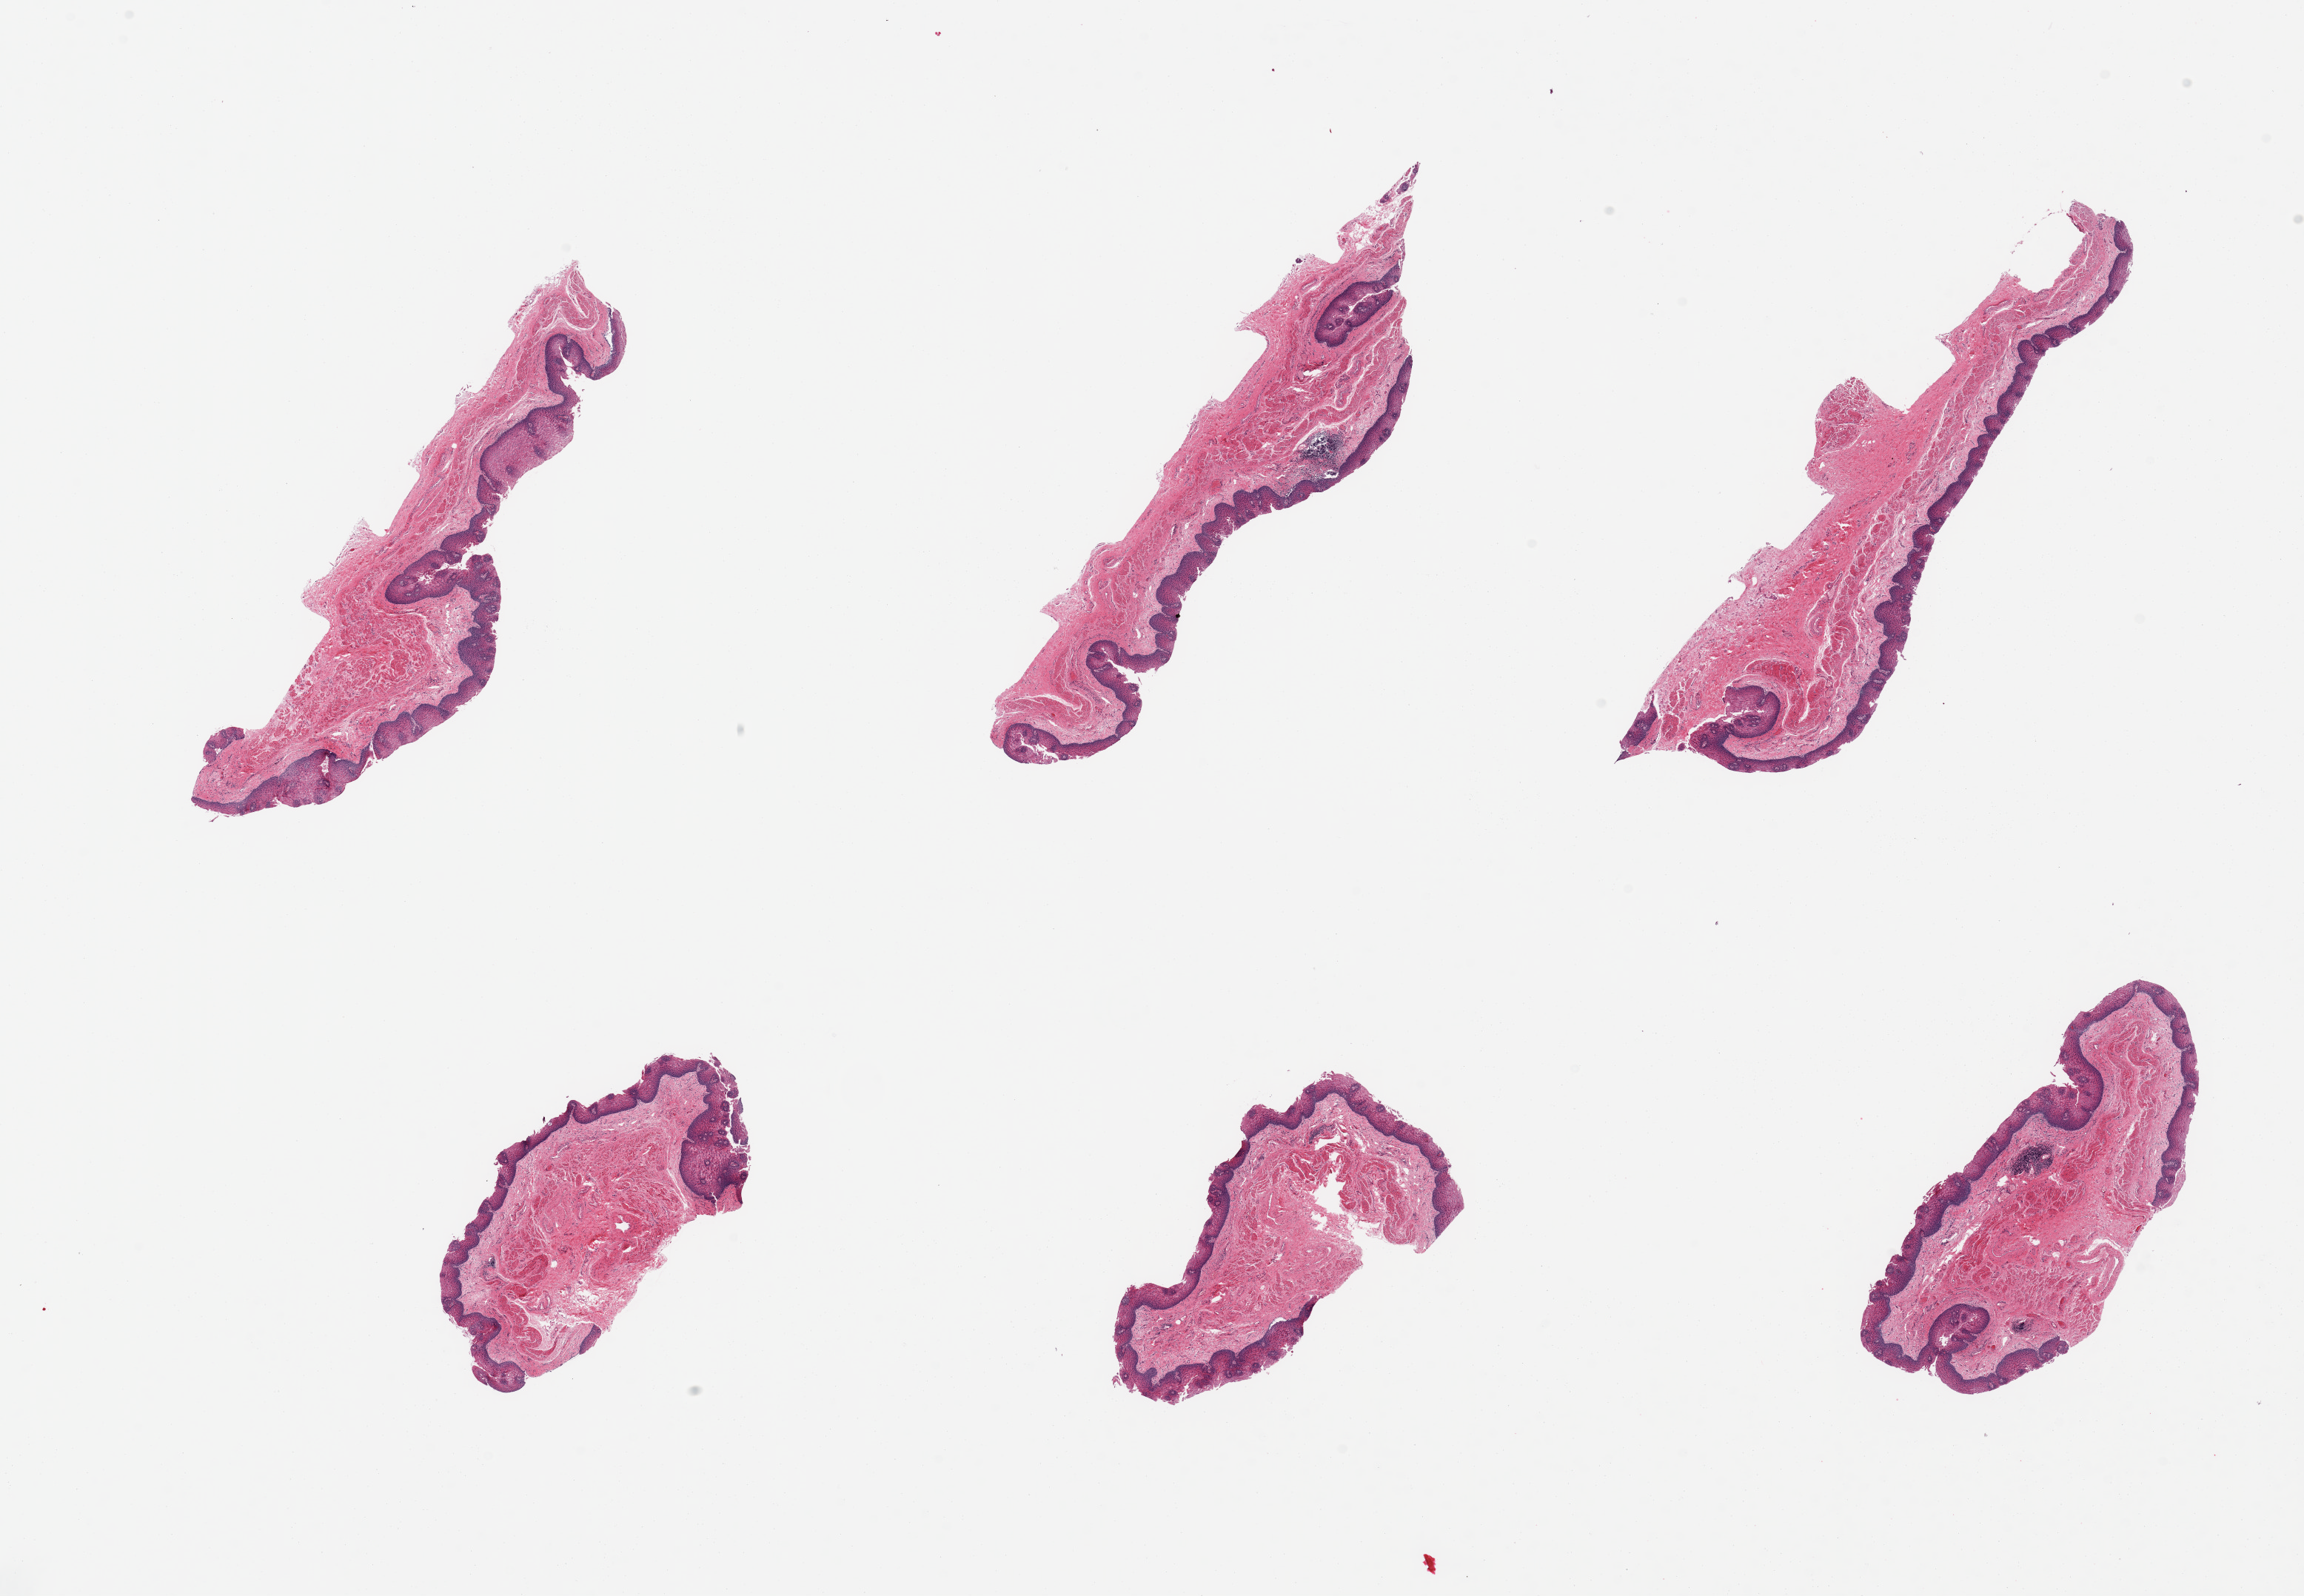
Whole-slide image, H&E stain, shown as a low-resolution overview of the whole scanned area (about 24.6 x 17.1 mm); PAXgene-fixed paraffin-embedded (PFPE) section; target tissue: esophageal mucous membrane; tissue donor sample. Donor: male.
Pathologist's review note for this sample: 6 pieces, sqaumous mucosa 0.3-0.4mm thick, ~20% total thickness.